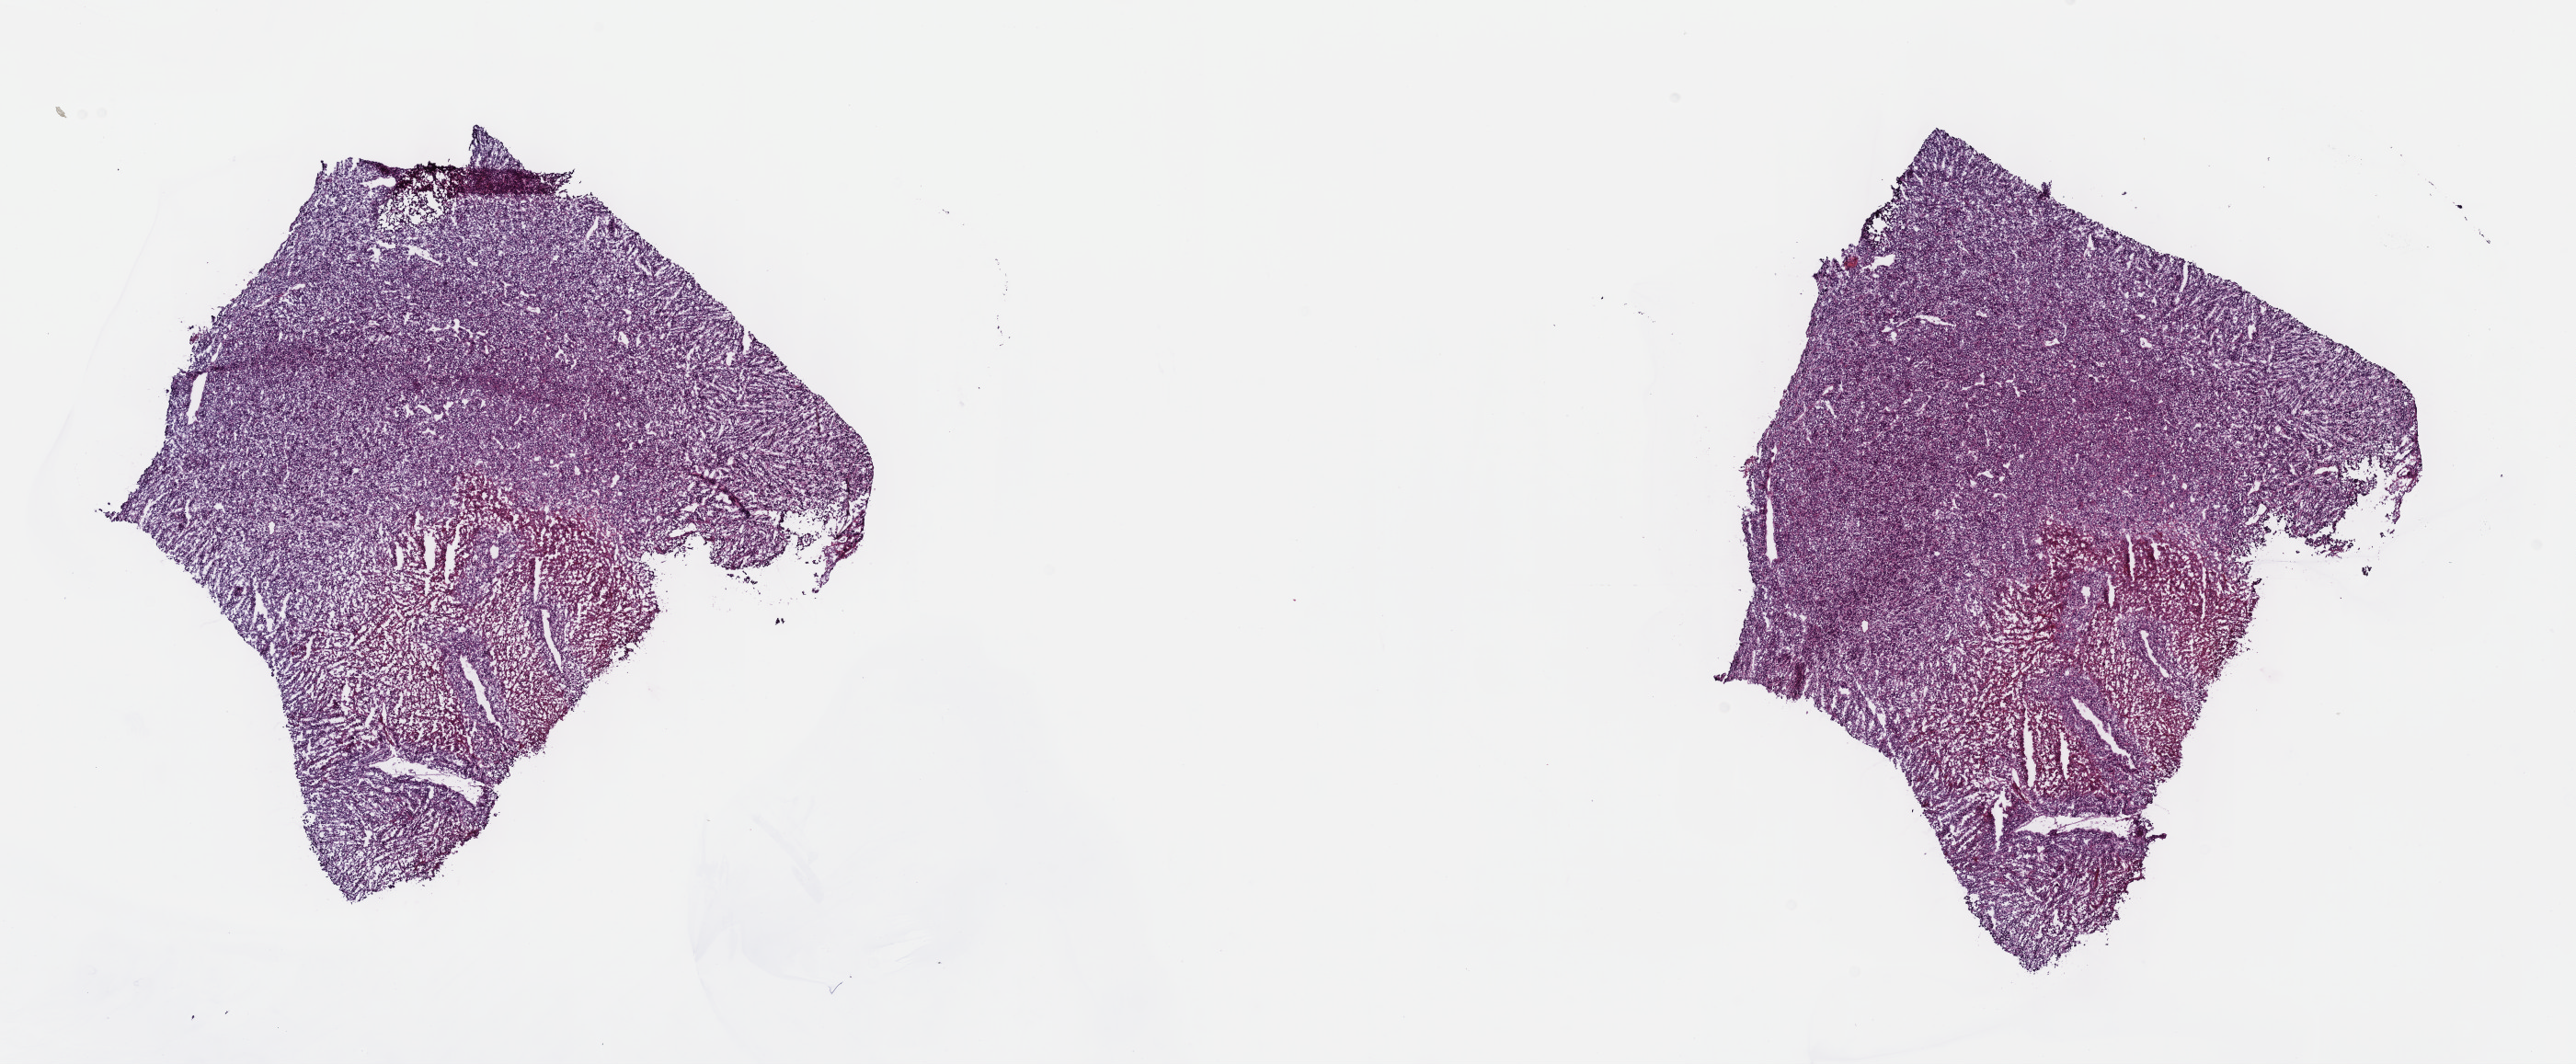
Whole-slide histology image, Hematoxylin and eosin (H&E) stained — shown as a low-resolution overview of the whole scanned area (about 22.7 x 9.4 mm, from a 40x scan); frozen section; sample: primary tumour, connective, subcutaneous and other soft tissues. Female, age 53 years at initial diagnosis. Slide review estimates, as recorded: tumour cells 80%, tumour nuclei 80%, normal cells 0%, stromal cells 12%, necrosis 8%. Infiltration values recorded for this section: lymphocyte infiltration 2%, monocyte infiltration 1%, neutrophil infiltration 2%.
Histologic diagnosis: Undifferentiated sarcoma (connective, subcutaneous and other soft tissues of pelvis).